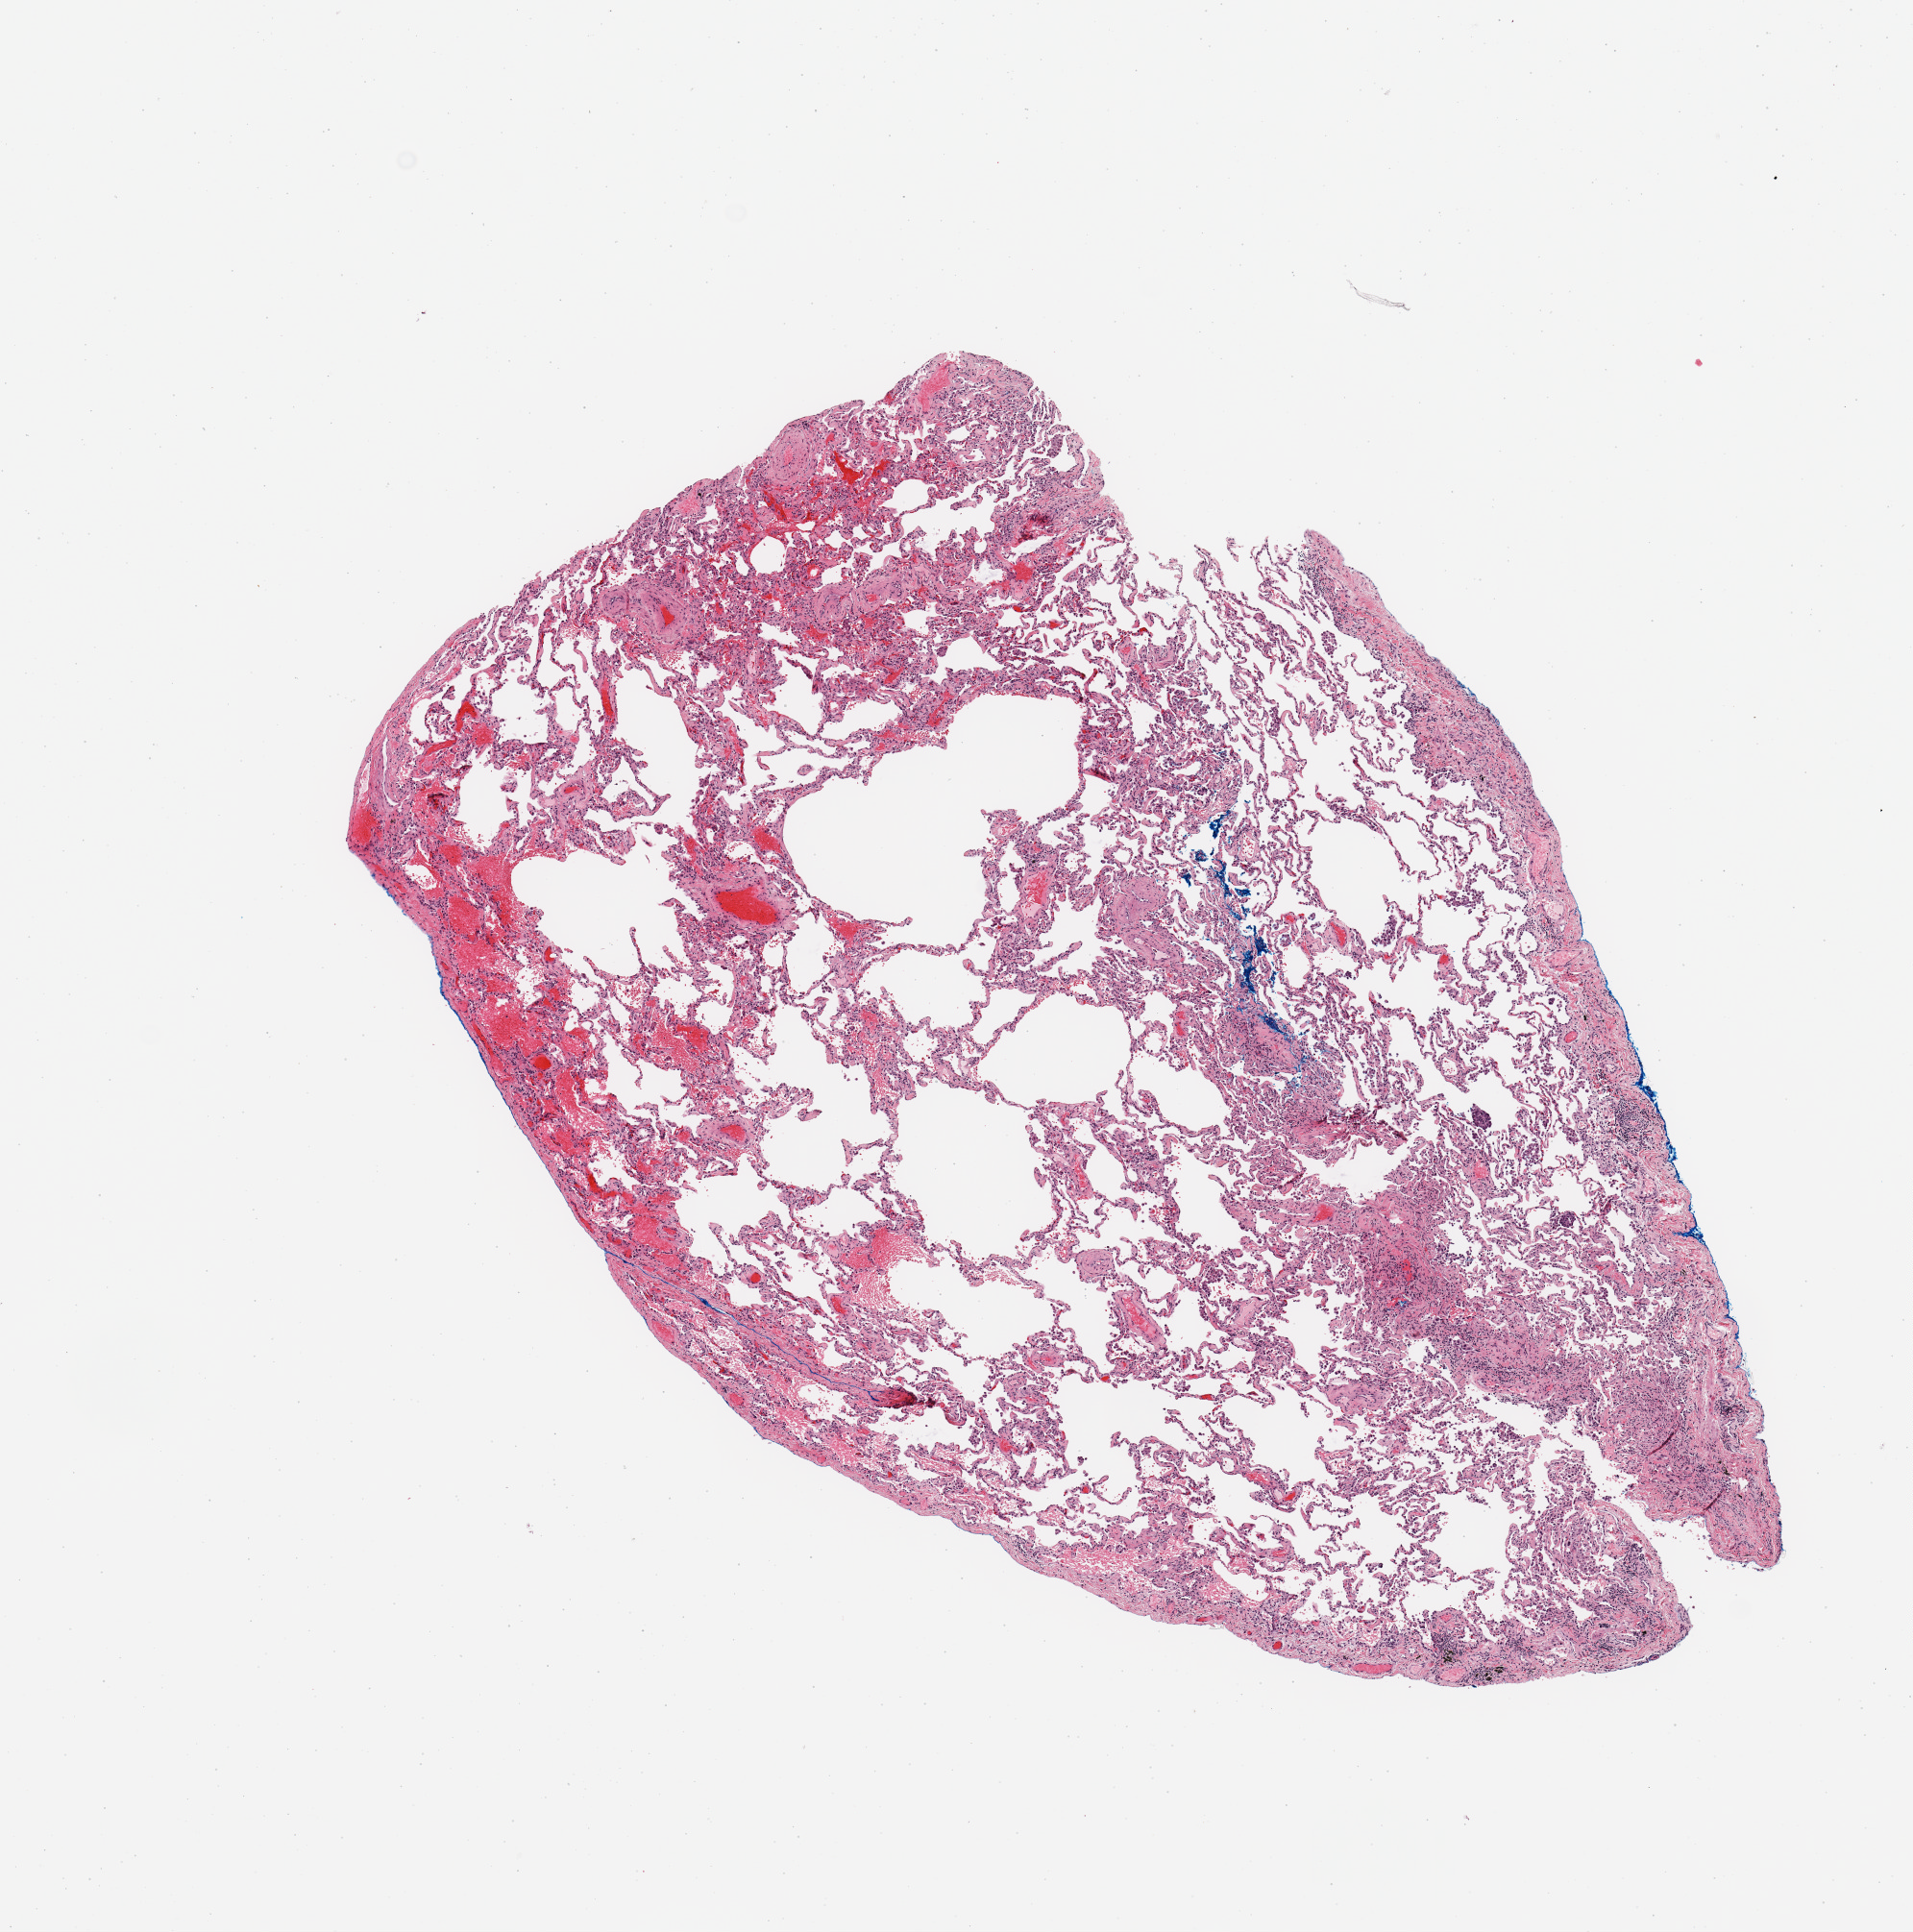
H&E whole-slide image, shown as a low-resolution overview of the whole scanned area (about 7.9 x 8.0 mm, acquisition: 20x scan); normal (non-tumour) tissue sample, sampled site: lung. Patient: male, age 77 years.
This section: normal (non-tumour) tissue from the same patient. Patient diagnosis: Adenocarcinoma, NOS.